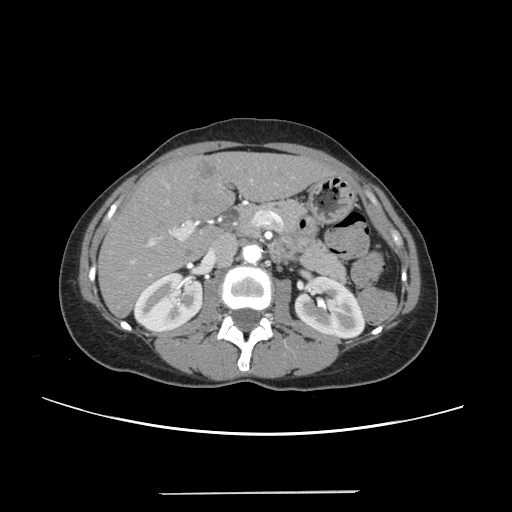
Contrast-enhanced abdominal CT, one axial slice. Position 123 of 240 along the scan axis. 120 kVp. Intravenous contrast given. Soft-tissue window (W 400 / L 40 HU). 1.25 mm slice thickness. 512 × 512 image matrix. Female patient, age 60 years. From the clinical record (not read from this slice): diagnosis: colorectal cancer liver metastases, imaged before liver resection; multiple liver metastases: no; largest metastasis: 1.5 cm; chemotherapy before resection: yes.
Structures marked on this image (expert manual segmentation):
- liver: bounding box (x1, y1, x2, y2) in pixels: (100, 153, 329, 315)
- planned liver remnant (the part of the liver to remain after resection): (100, 154, 330, 315)
- portal vein (with intrahepatic branches): (130, 179, 278, 276)
- liver metastasis: (196, 161, 218, 180)